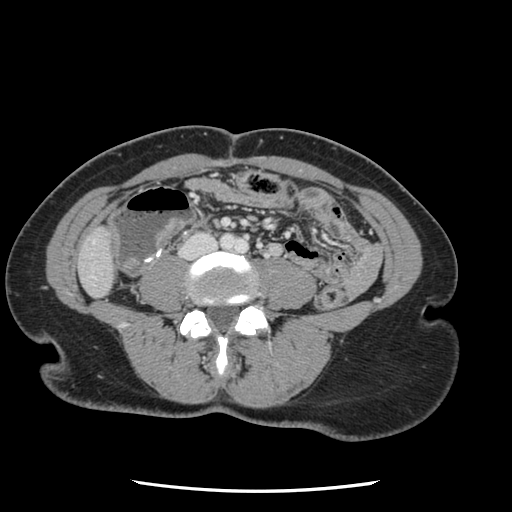
Contrast-enhanced abdominal CT, one axial slice; position 1 of 134 along the scan axis; 120 kVp; intravenous contrast given; soft-tissue window (W 400 / L 40 HU); 2.5 mm slice thickness; 512 × 512 image matrix. Female patient, age 43 years. From the clinical record (not read from this slice): diagnosis: colorectal cancer liver metastases, imaged before liver resection; multiple liver metastases: yes; largest metastasis: 3.4 cm.
Annotated regions visible in this slice (outlined manually by an expert reader):
- liver: bounding box (x1, y1, x2, y2) in pixels: (81, 228, 114, 297)
- planned liver remnant (the part of the liver to remain after resection): (81, 229, 114, 297)